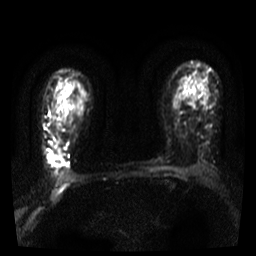
Breast MRI, one axial slice. Slice 26 of 36 in the series (ordered by position). Diffusion-weighted series; image 2 of 4 stored at this slice position (different b-values; order by instance number). 3 T. 256 × 256 image matrix, field of view 300 × 300 mm. Female patient.
Annotated regions visible in this slice (manually delineated by an expert):
- tumour on diffusion-weighted imaging: bounding box [x1, y1, x2, y2] px = [47, 155, 59, 165]